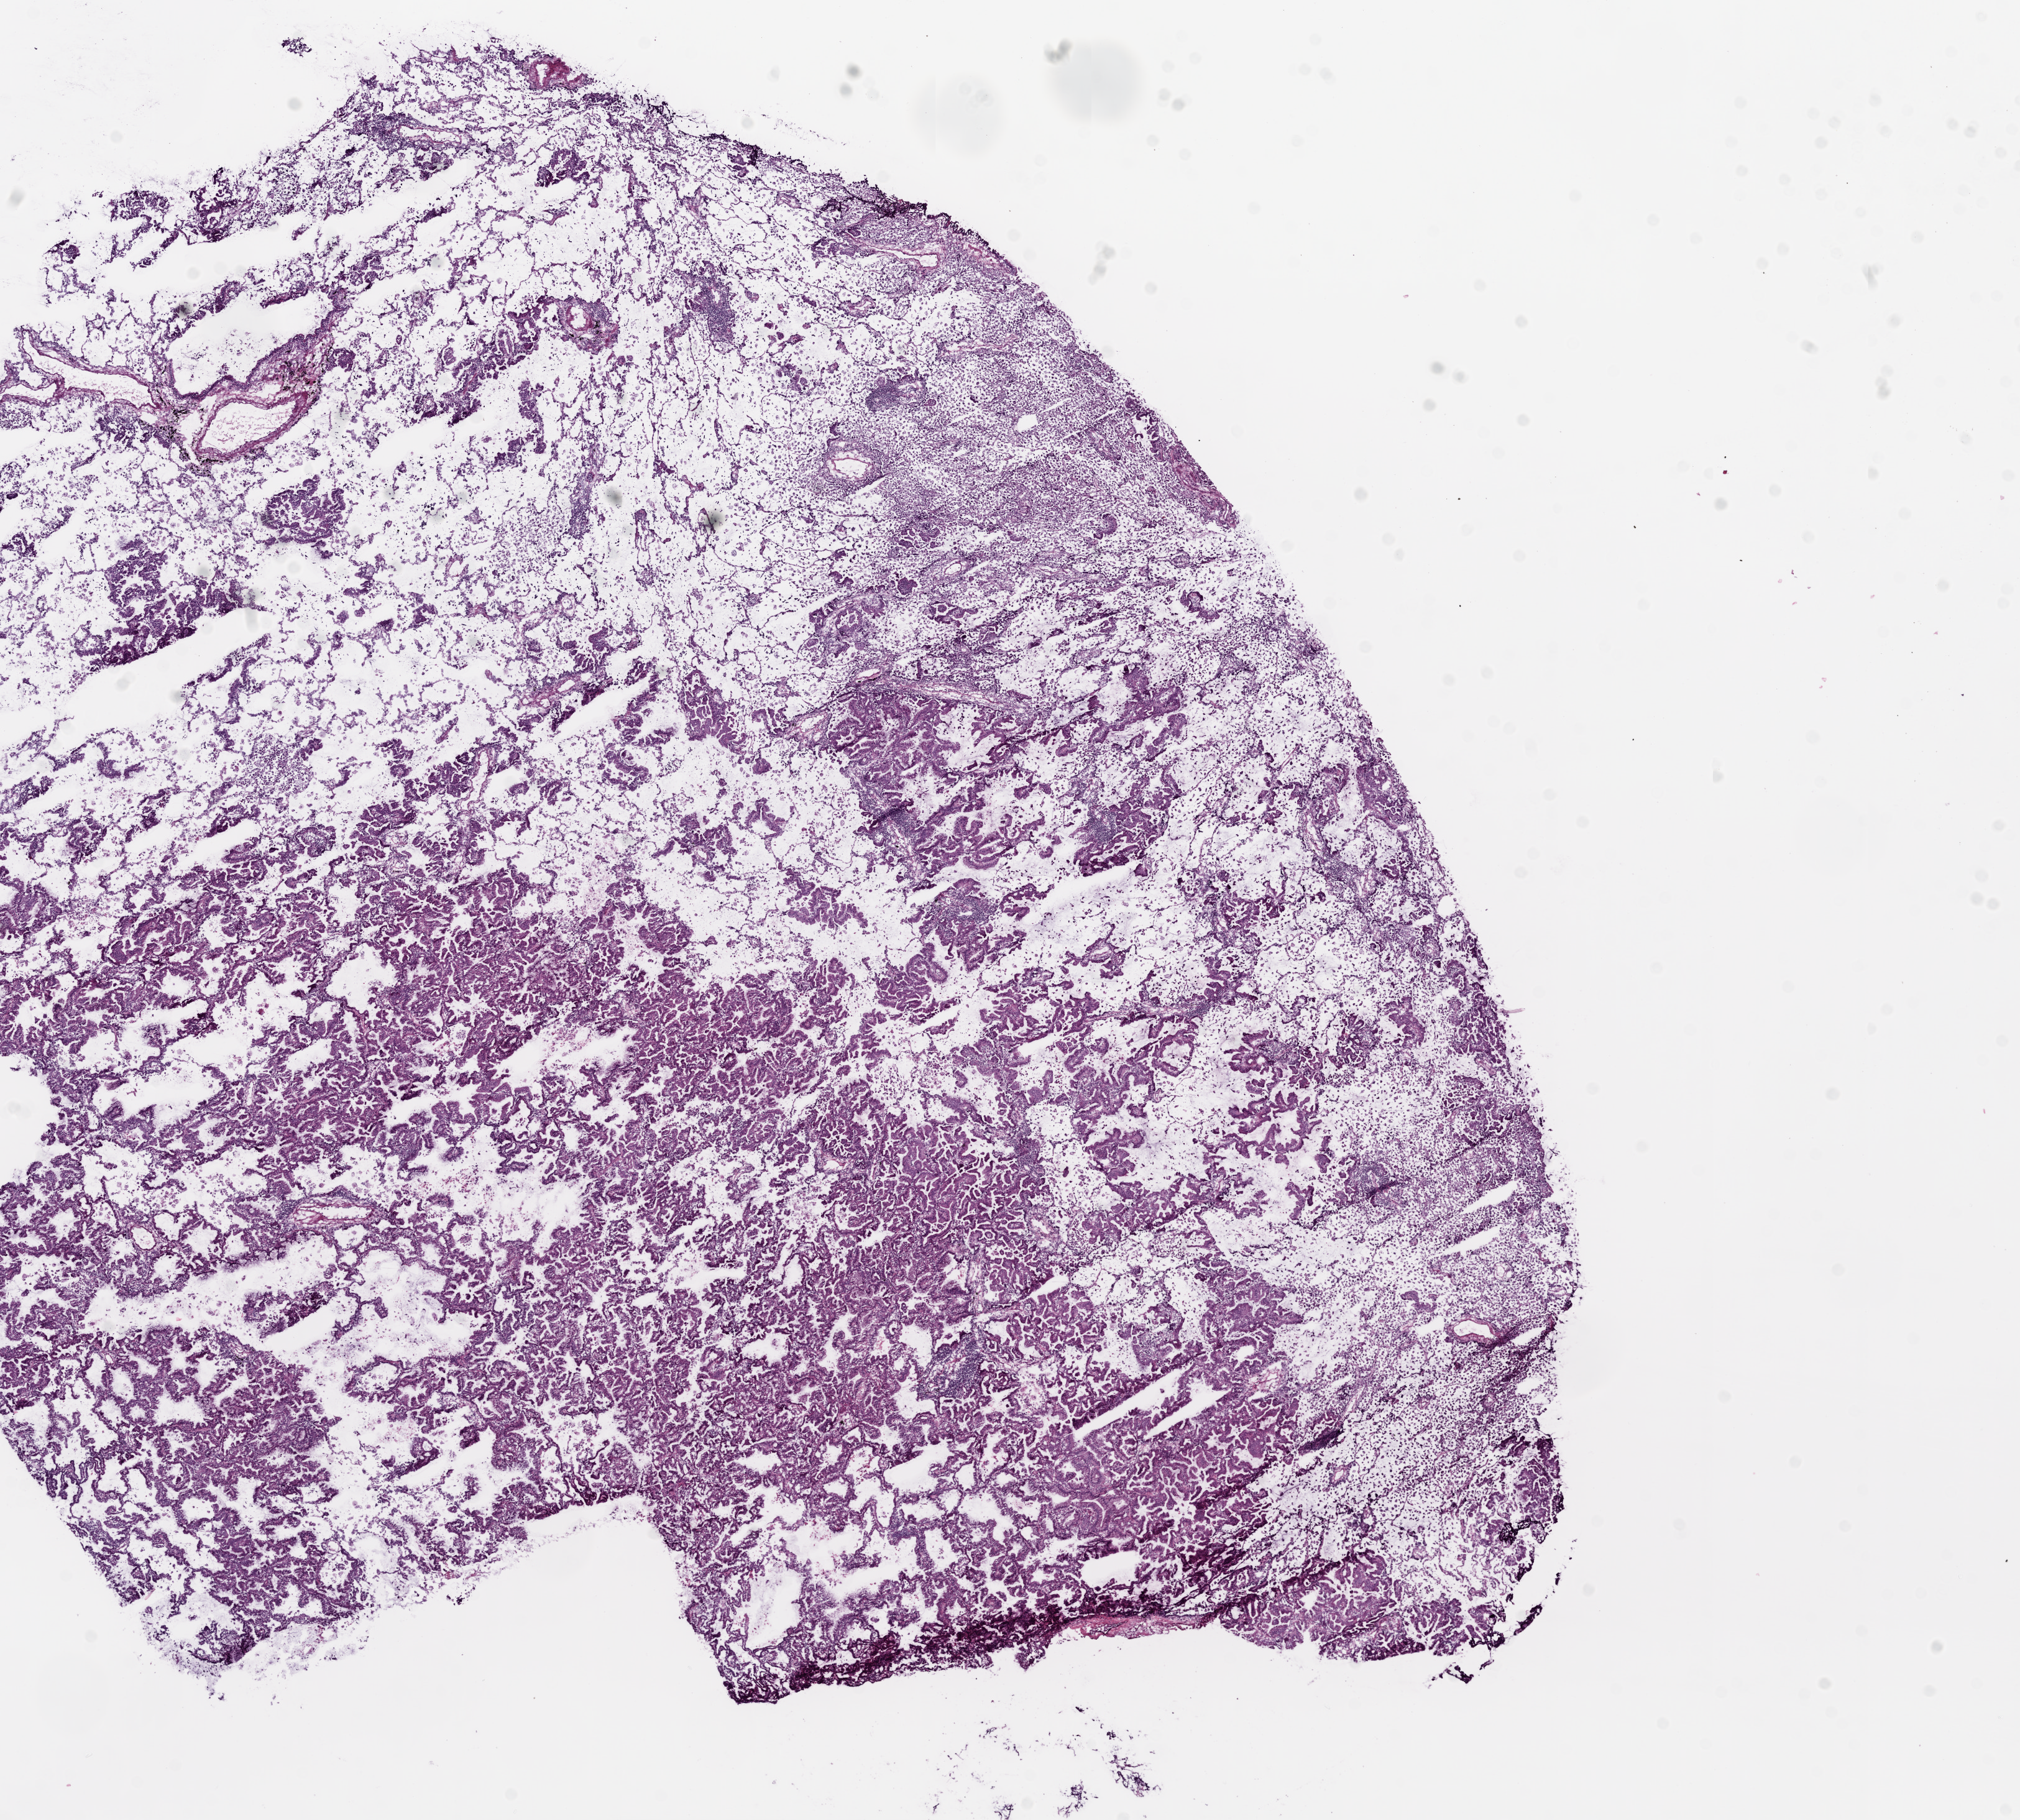
H&E whole-slide image, shown as a low-resolution overview of the whole scanned area (about 13.0 x 11.7 mm, slide scanned at 20x). Frozen section. Primary tumour sample from the lung. Male patient; age at initial diagnosis 82 years. Composition of this section per pathologist review: tumour cells 70%, tumour nuclei 70%, normal cells 20%, stromal cells 10%, necrosis 0%.
* AJCC pathologic stage: IB (6th edition)
* laterality: left
* pathologic diagnosis: Adenocarcinoma with mixed subtypes (lower lobe, lung)